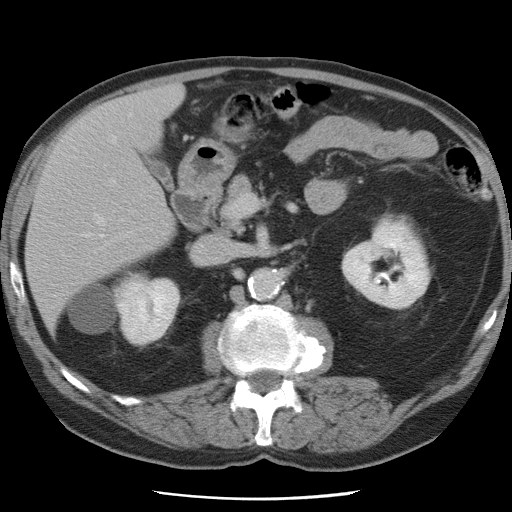
Contrast-enhanced abdominal CT, one axial slice. Slice 36 of 78 in the series (ordered by position). 120 kVp. Intravenous contrast given. Soft-tissue window (W 400 / L 40 HU). 5 mm slice thickness. 512 × 512 image matrix, field of view 337 × 337 mm. Male patient, age 75 years. From the clinical record (not read from this slice): diagnosis: colorectal cancer liver metastases, imaged before liver resection; multiple liver metastases: yes; largest metastasis: 2.4 cm; chemotherapy before resection: yes.
Structures marked on this image (outlined manually by an expert reader):
- hepatic veins: bounding box (x1, y1, x2, y2) in pixels: (80, 114, 131, 241)
- liver: (25, 85, 183, 324)
- planned liver remnant (the part of the liver to remain after resection): (26, 117, 174, 326)
- portal vein (with intrahepatic branches): (110, 180, 114, 183)